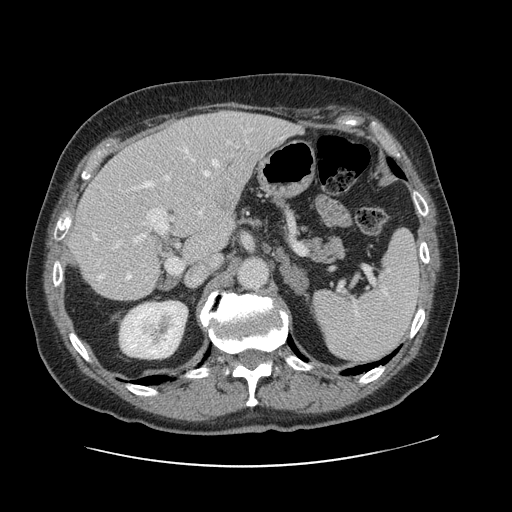
Contrast-enhanced abdominal CT, one axial slice; position 70 of 138 along the scan axis; 120 kVp; soft-tissue window (W 400 / L 40 HU); 2.5 mm slice thickness; 512 × 512 image matrix, field of view 402 × 402 mm. Male patient, age 71 years. Case-level facts recorded for this patient, not image findings: diagnosis: colorectal cancer liver metastases, imaged before liver resection.
Annotated regions visible in this slice (outlined manually by an expert reader):
- hepatic veins: box from (x=93, y=149) to (x=223, y=280) px
- liver: (x=72, y=113)–(x=295, y=300)
- planned liver remnant (the part of the liver to remain after resection): (x=71, y=146)–(x=225, y=300)
- portal vein (with intrahepatic branches): (x=112, y=132)–(x=248, y=274)
- liver metastasis: (x=212, y=190)–(x=237, y=214)